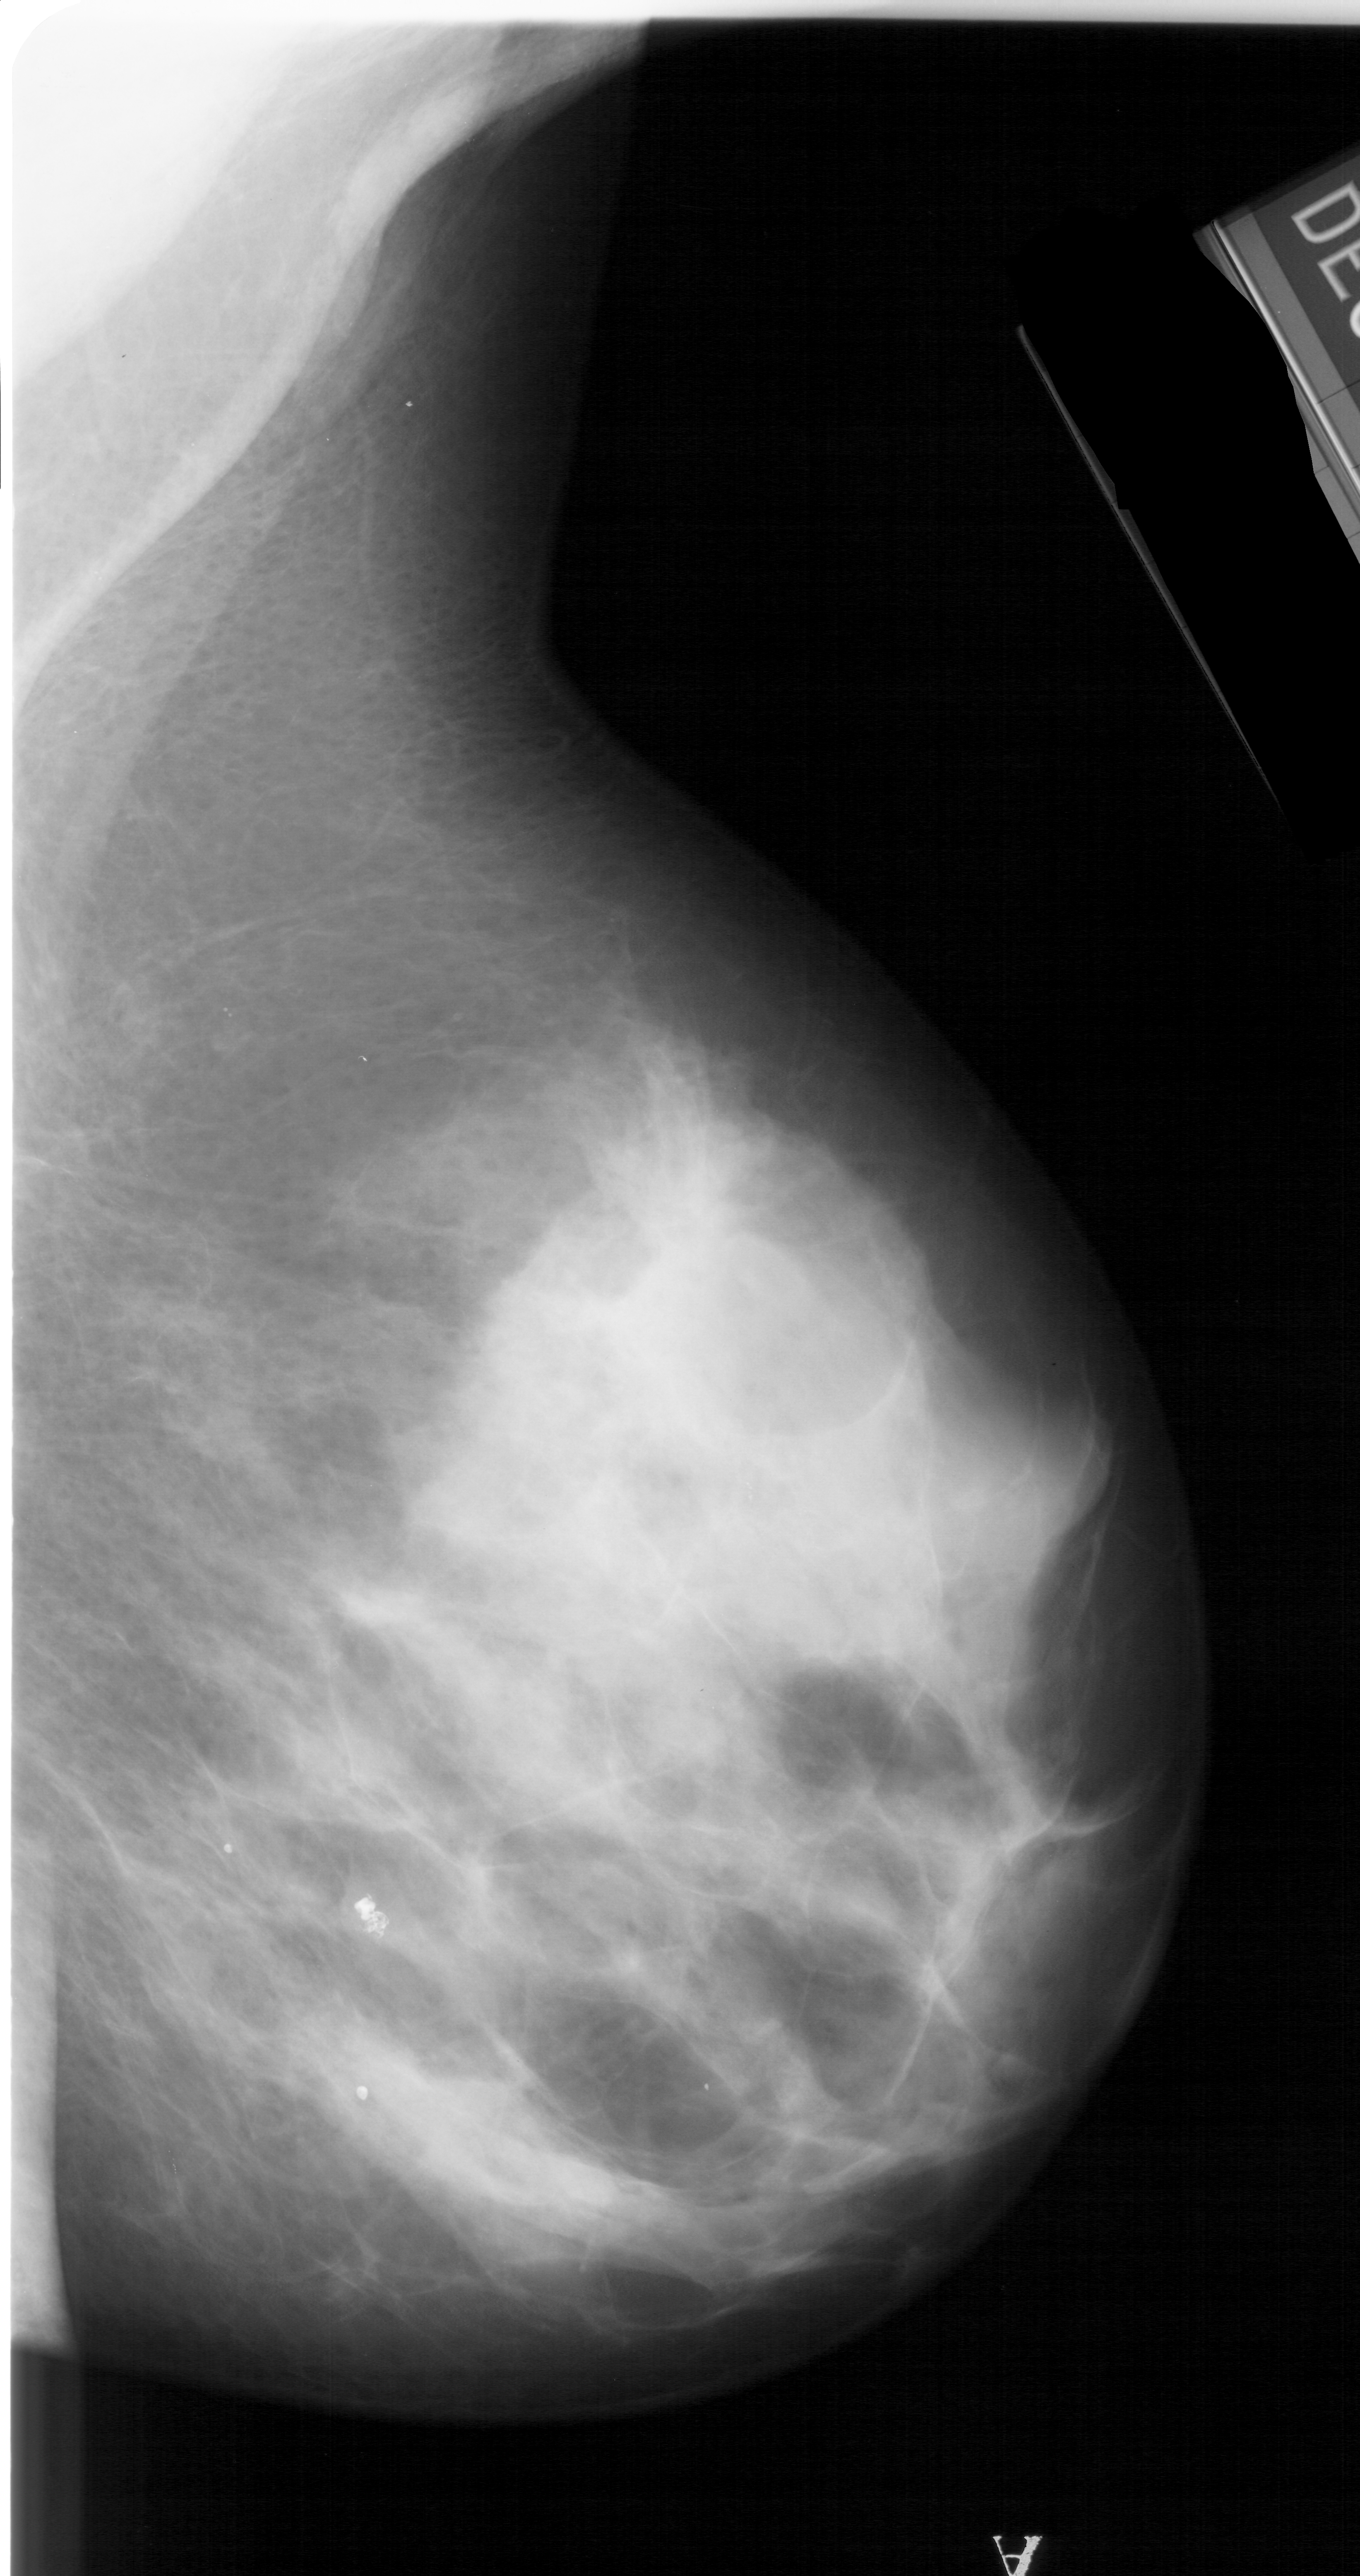
Mammogram (digitized film); right breast; MLO view; breast composition: extremely dense (BI-RADS density category 4 of 4).
- Abnormality record for this image: calcifications, morphology punctate, distribution clustered; BI-RADS assessment category 3; subtlety rating 1 on a 1 (subtle) to 5 (obvious) scale; pathology result (as recorded, not read from the image): malignant.